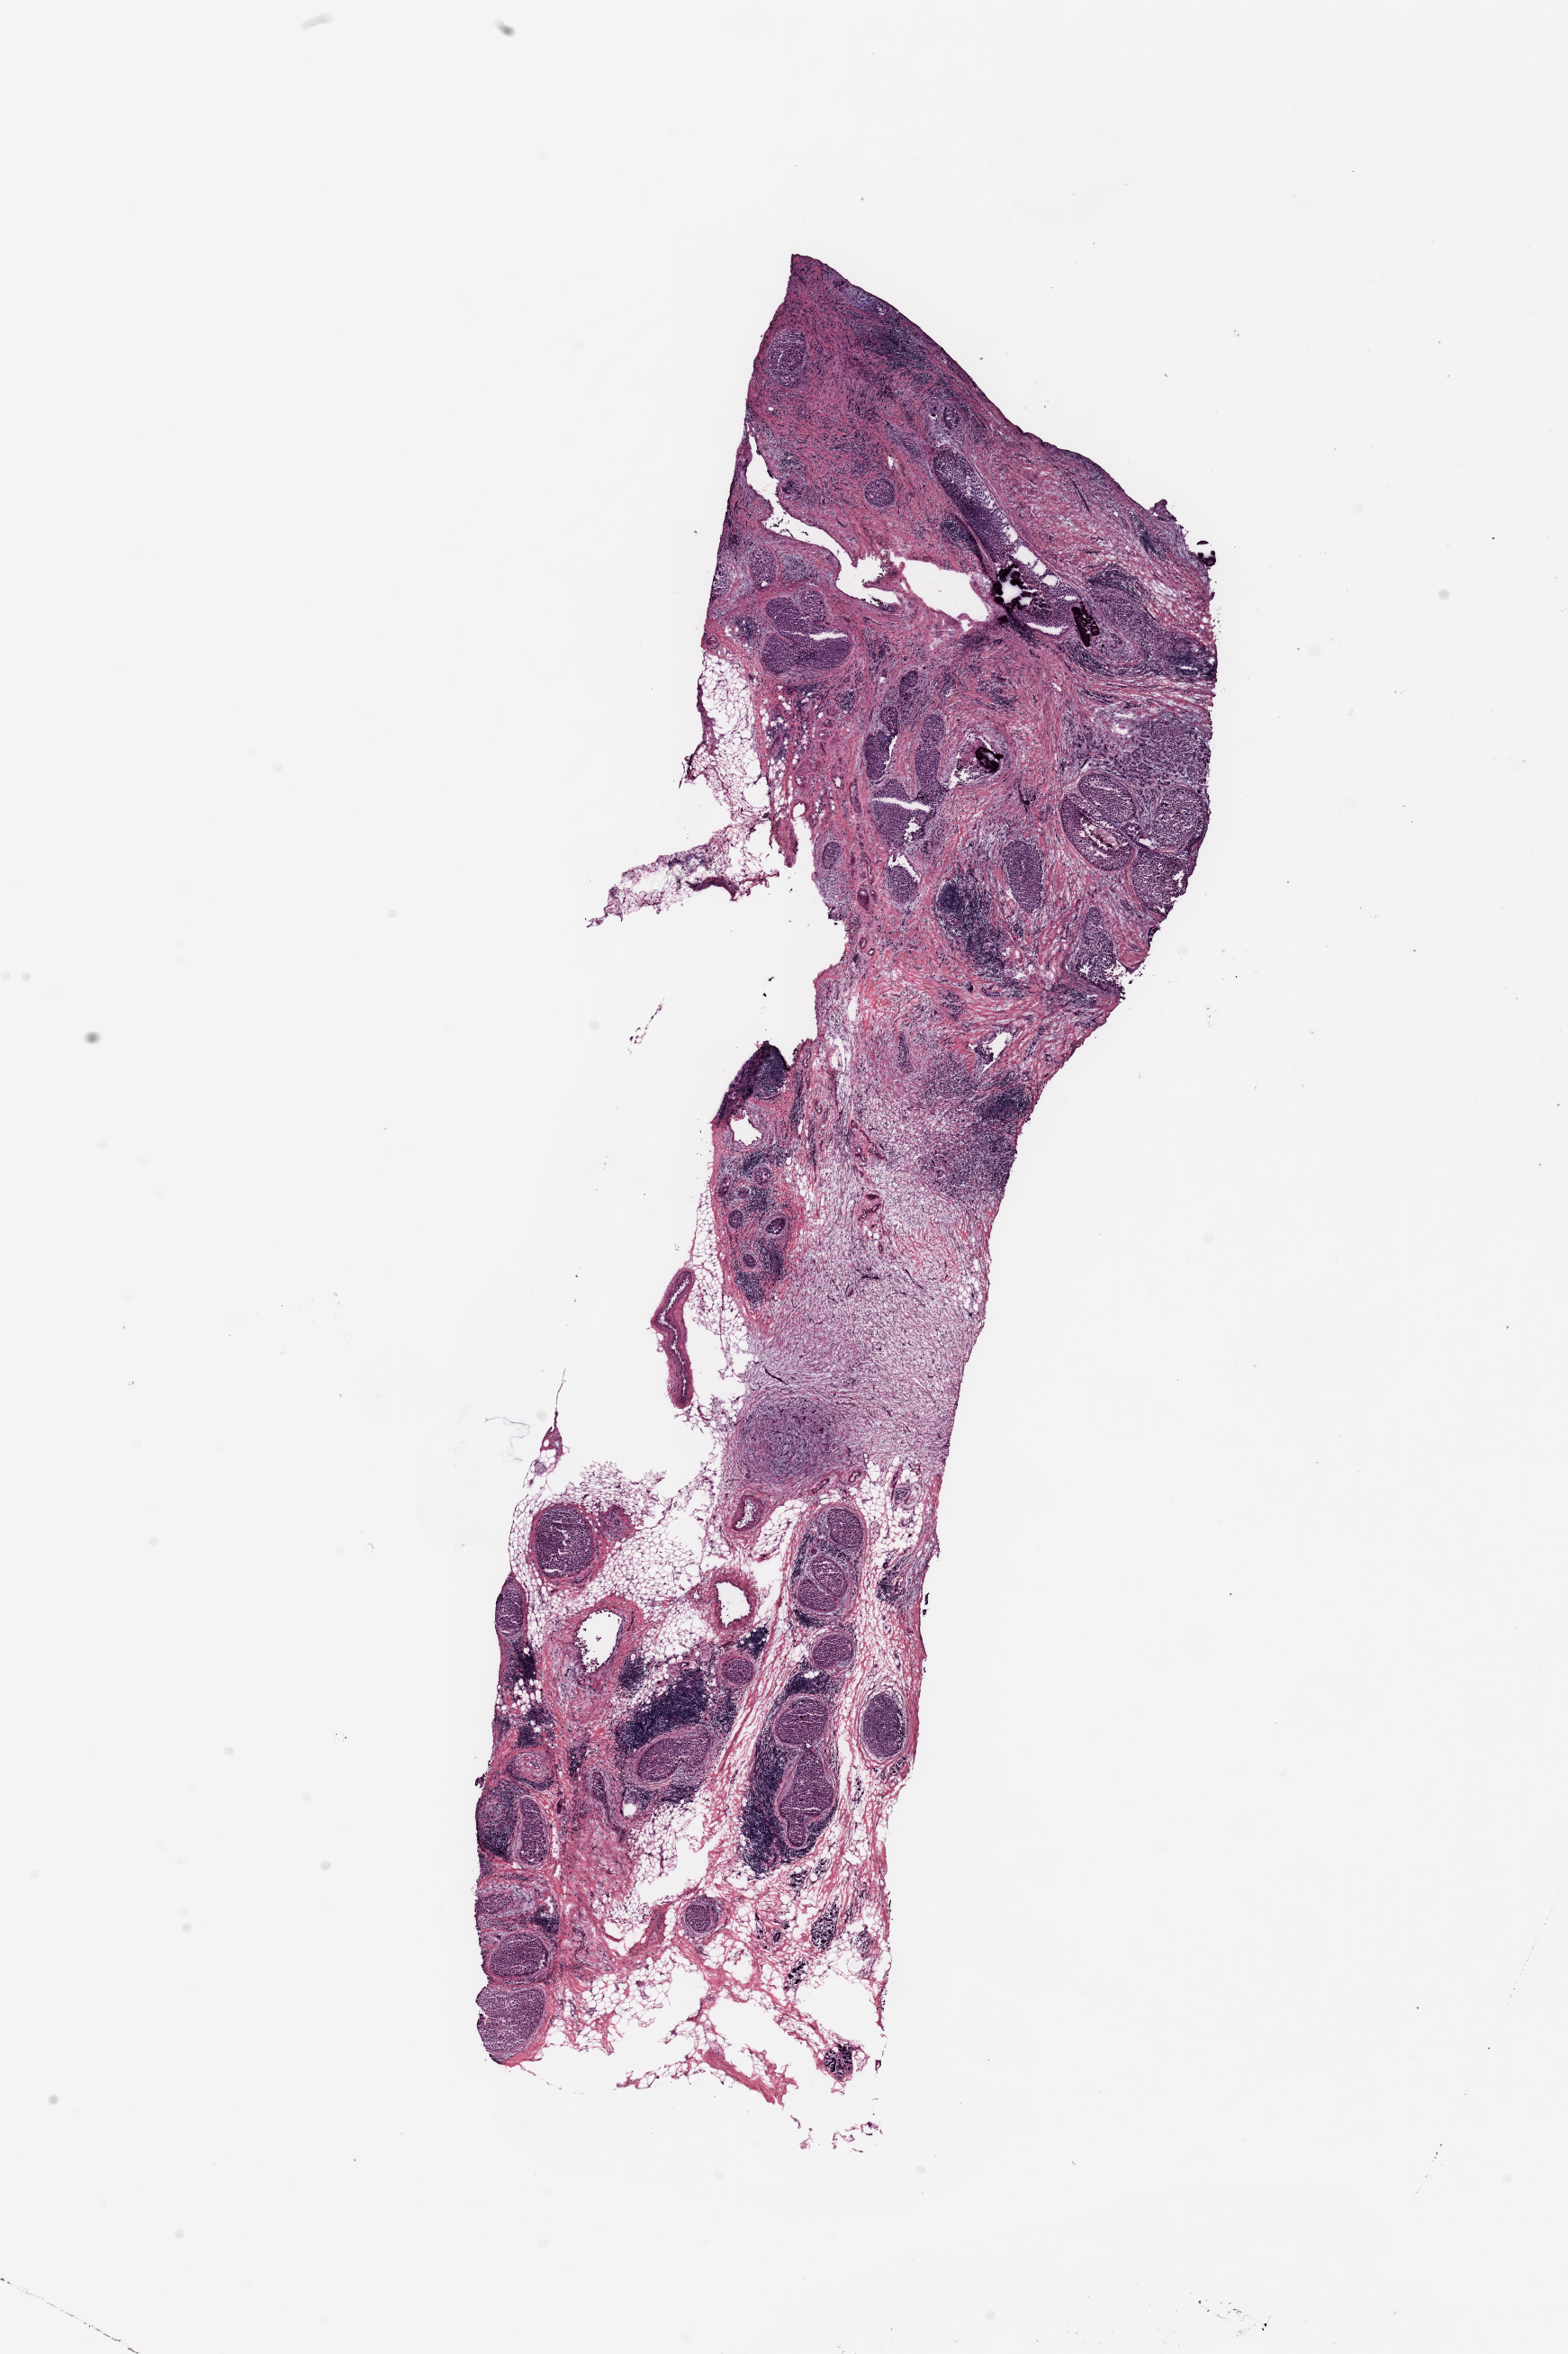
Whole-slide histology image, H&E, whole scanned area (about 13.8 x 20.7 mm, acquisition: 20x scan) shown as a low-resolution overview, breast, tissue type not recorded.
Patient diagnosis (cohort enrolment): breast cancer (breast).